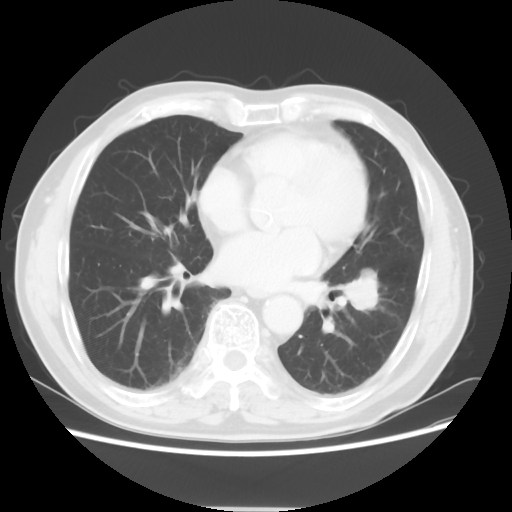
Chest CT, one axial slice. Lung window (W 1500 / L -600 HU). 512 × 512 image matrix, field of view 366 × 366 mm. Patient: male, 71 years. Case-level facts recorded for this patient, not image findings: clinical TNM (as recorded): T1c N1 M0.
Structures marked on this image (bounding box drawn by a radiologist):
- lung tumour (recorded histology: adenocarcinoma): bounding box (x1, y1, x2, y2) in pixels: (337, 258, 386, 324)